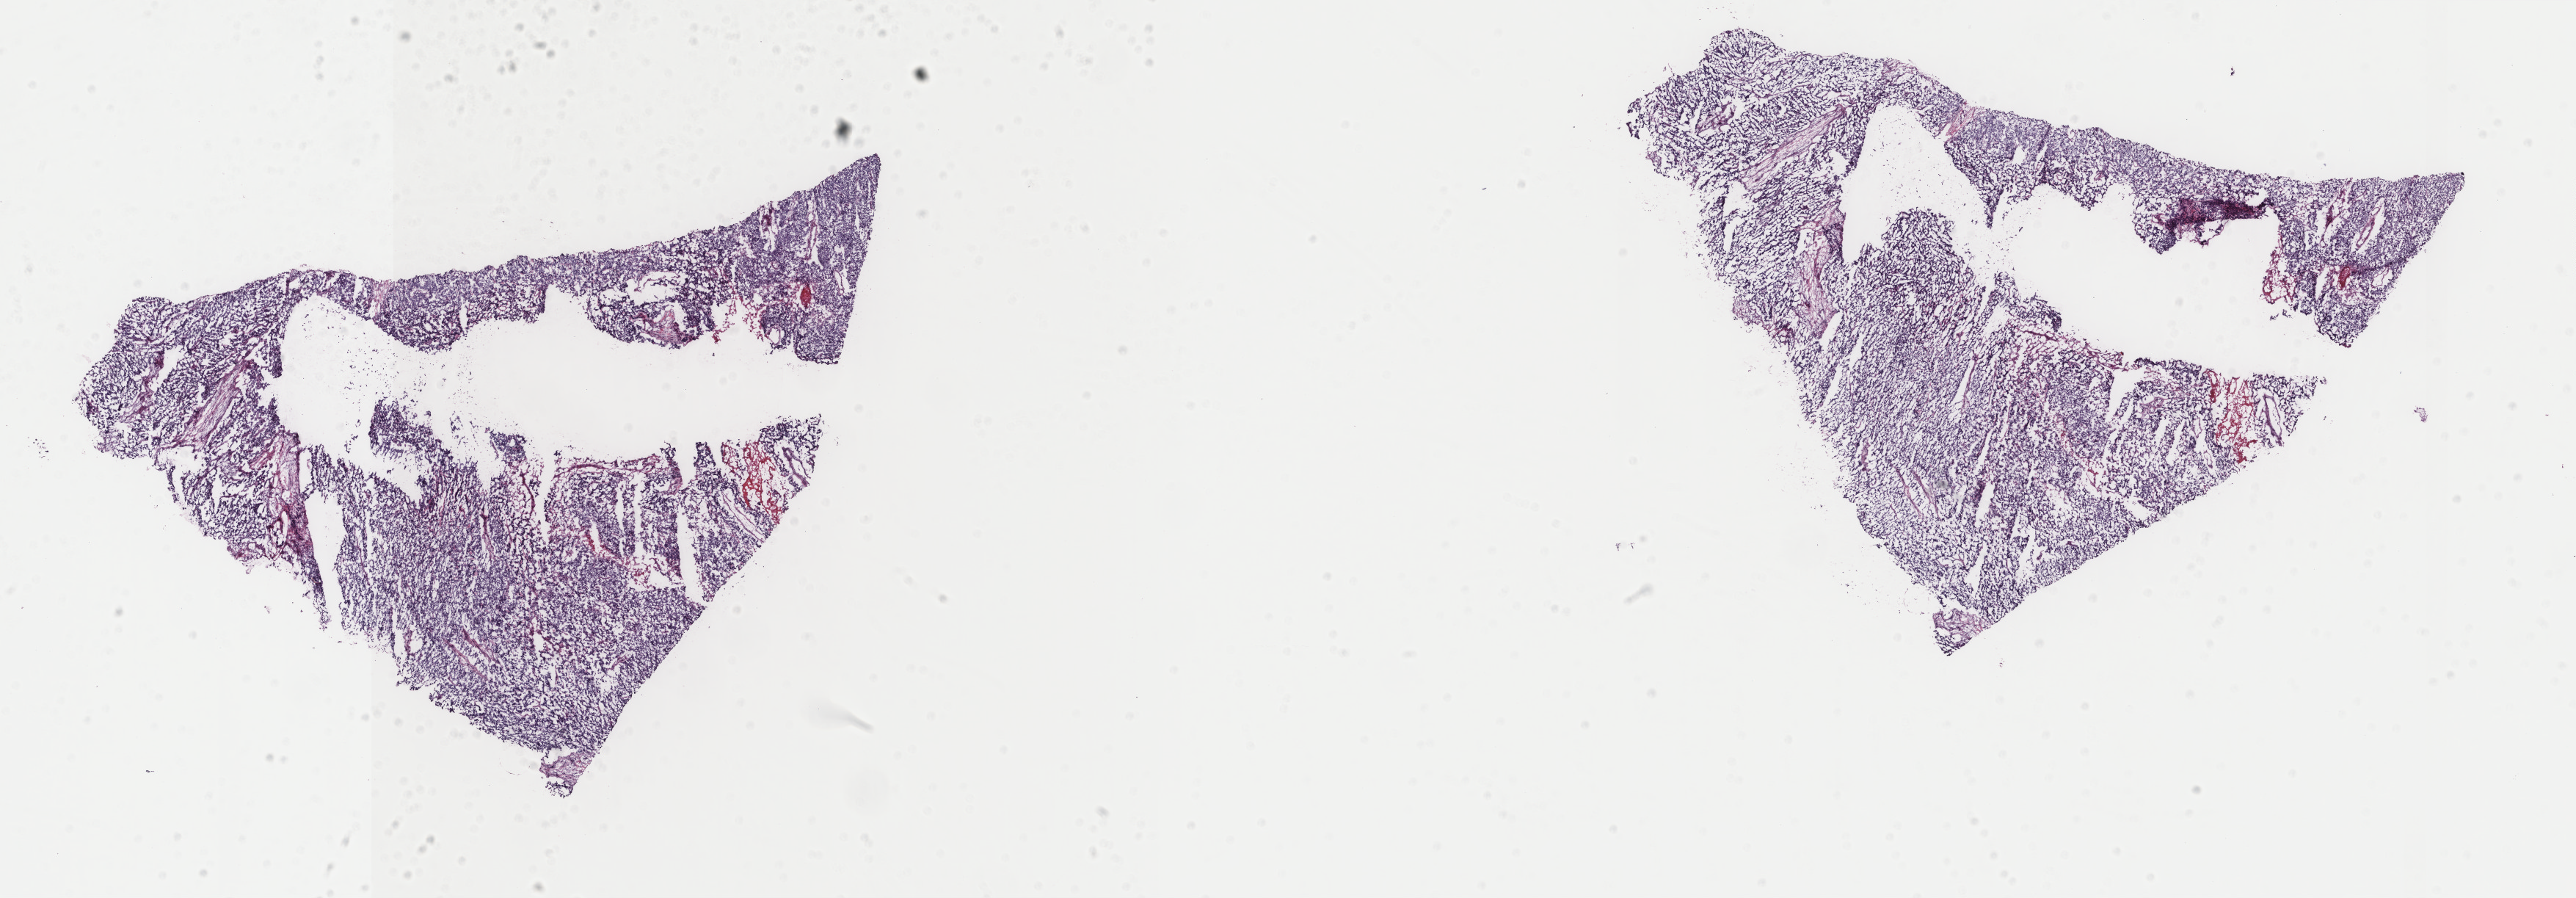
Digitized Hematoxylin and eosin (H&E) stained tissue section (whole slide) — low-resolution overview of the scanned area, about 27.9 x 9.7 mm; frozen section from the top of the tissue portion; uterus, primary tumour sample. Patient: female, age at initial diagnosis 33 years.
Histologic diagnosis: Endometrioid adenocarcinoma, NOS (endometrium).